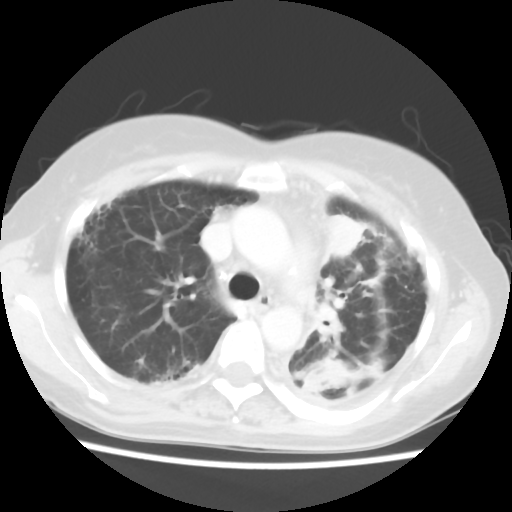
Chest CT, one axial slice; lung window (W 1500 / L -600 HU); 5 mm slice thickness; 512 × 512 image matrix. Female patient, age 56 years. From the clinical record (not read from this slice): clinical TNM (as recorded): T1c N0 M1.
Annotated regions visible in this slice (rectangle marked by the reading radiologist):
- lung tumour (recorded histology: adenocarcinoma): bounding box <316,206,369,263> (left, top, right, bottom; pixels)